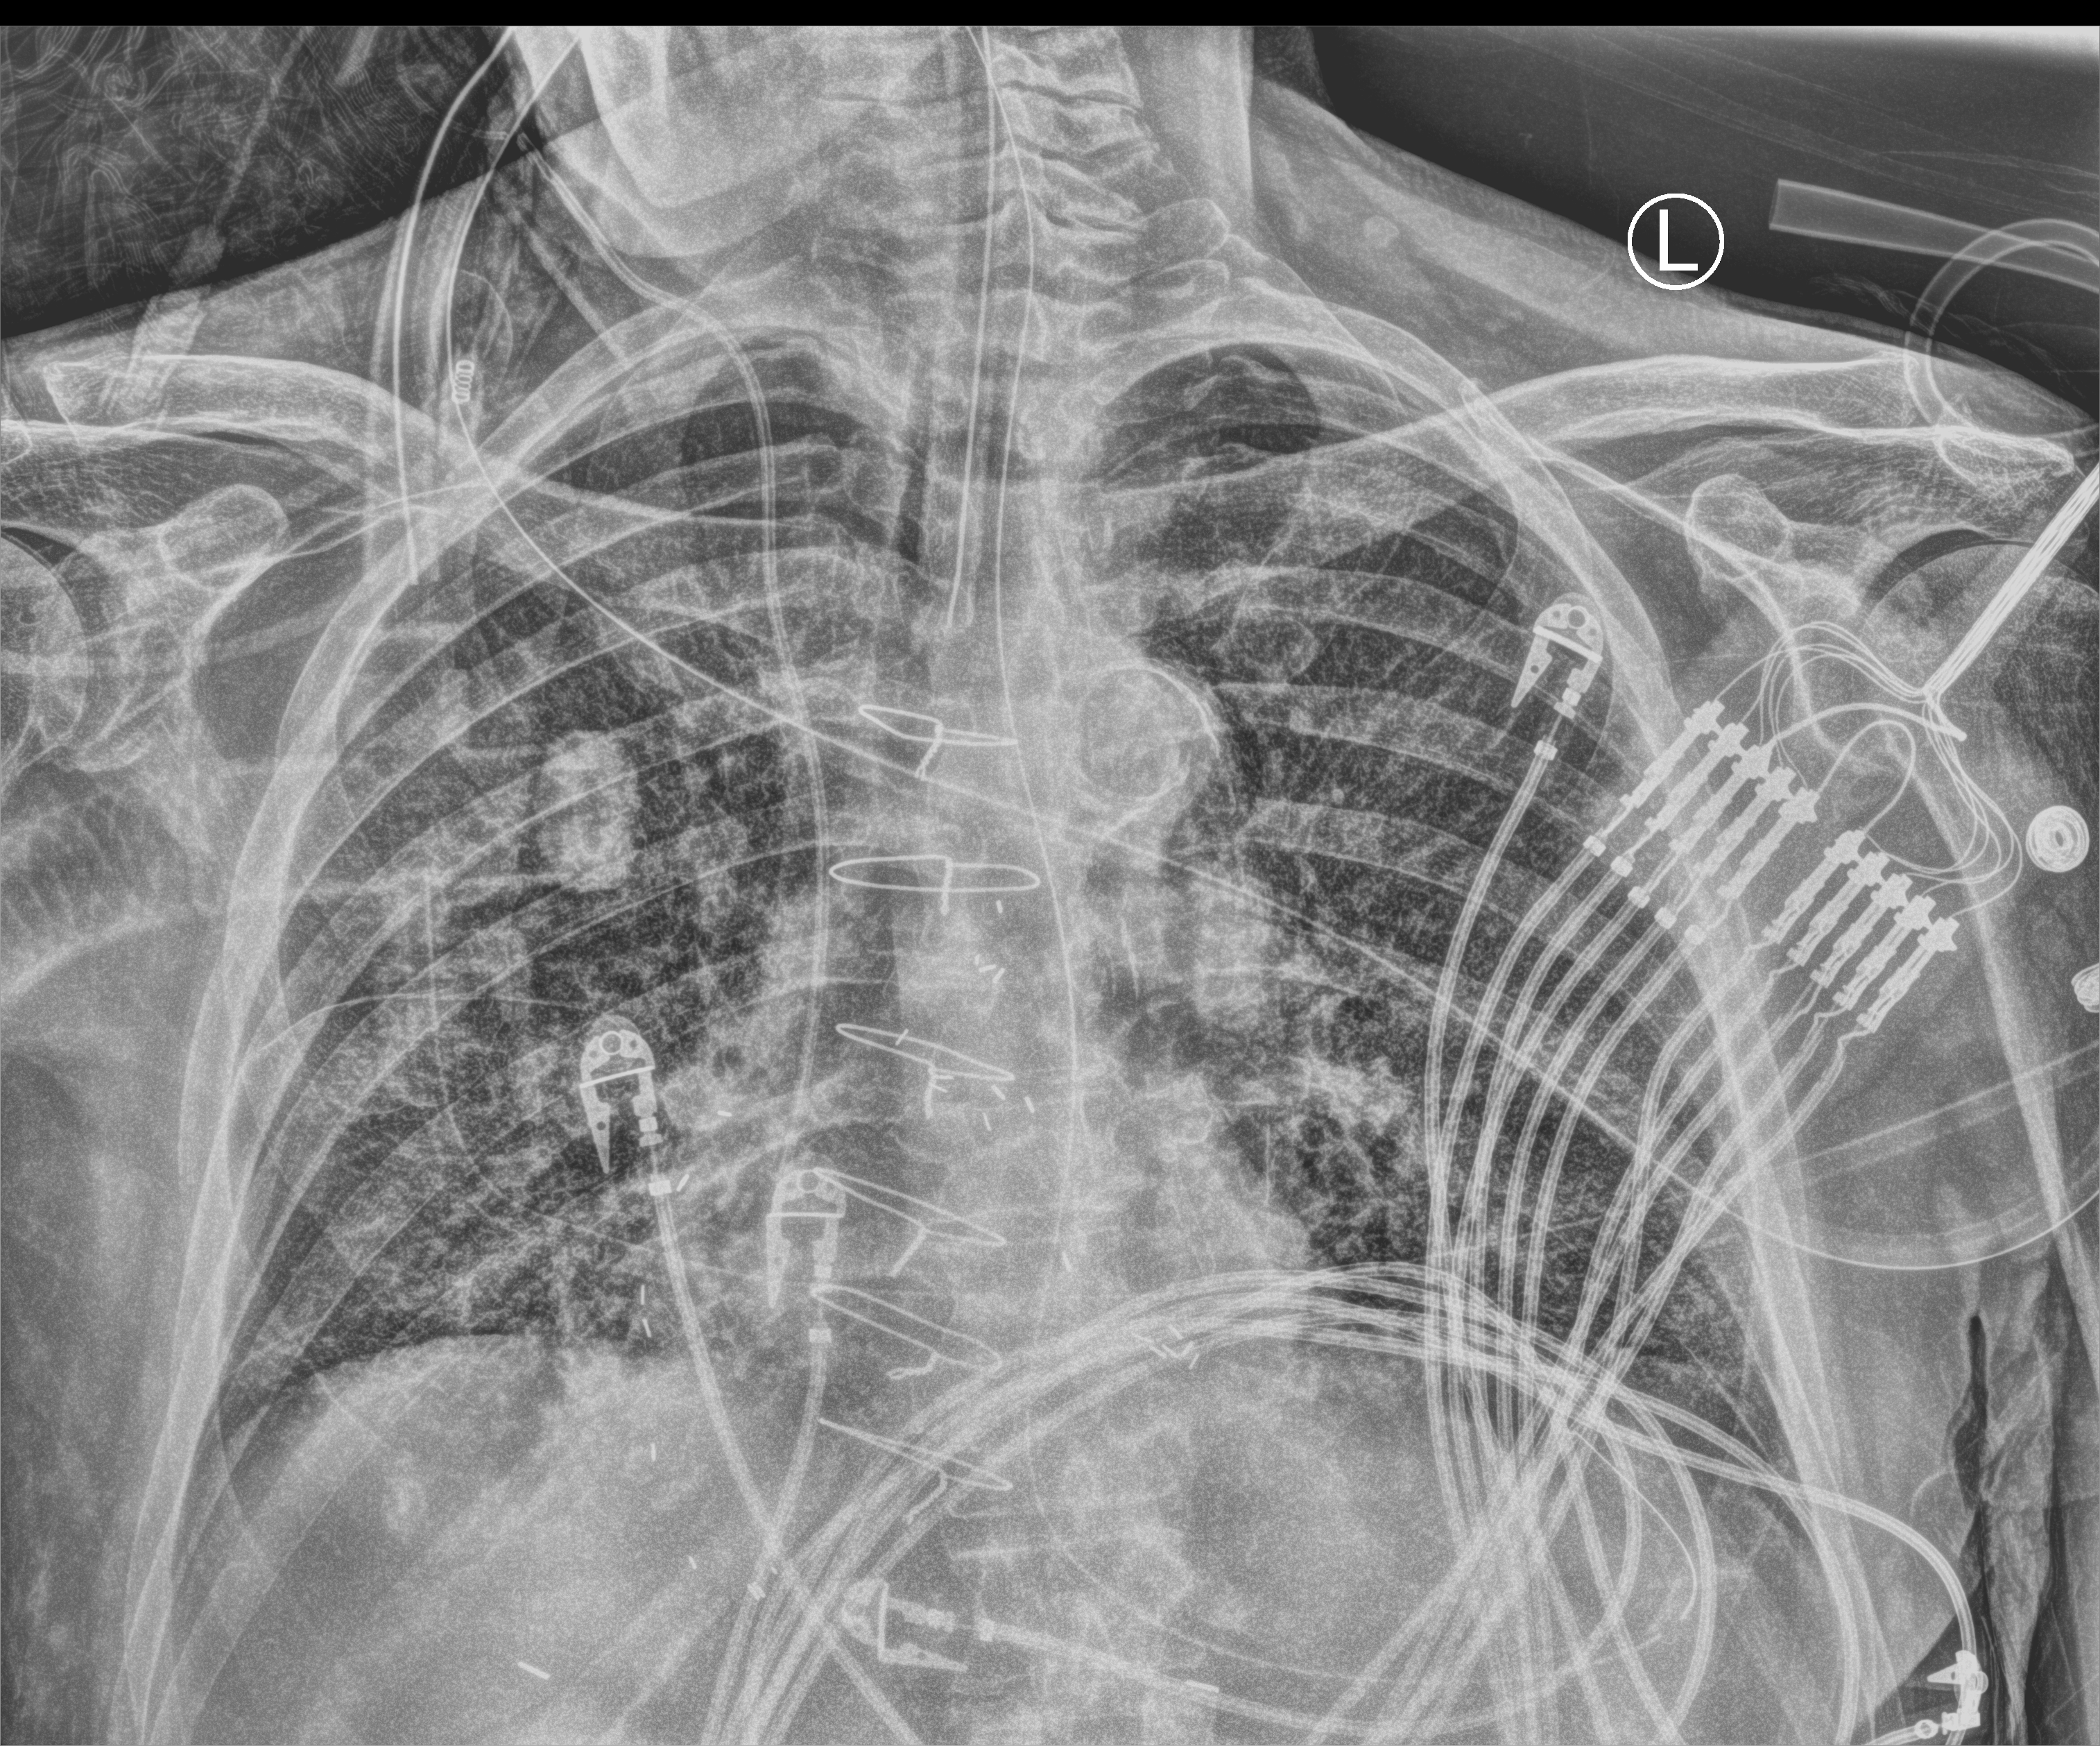
Portable chest radiograph; anteroposterior (AP) projection. Patient hospitalised with COVID-19; male, aged 75–90 years.
Hospital-stay facts (about this admission, not read from this image; timing relative to this image not recorded): mechanically ventilated during this hospital stay: yes; admitted to intensive care during this hospital stay: yes.